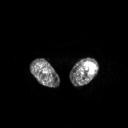
FDG PET of an extremity soft-tissue mass (from a PET/CT study), one axial slice; slice 196 of 267 in the series (ordered by position); 3.27 mm slice thickness; 128 × 128 image matrix, field of view 700 × 700 mm. Female patient, age 62 years. Case-level facts recorded for this patient, not image findings: histological type: undifferentiated – high grade; grade: high; site of the primary tumour: left thigh.
Outlined on this slice (expert contour drawn on MRI and transferred to this co-registered scan by the dataset authors):
- gross tumour volume including surrounding oedema: bounding box (x1, y1, x2, y2) in pixels: (85, 62, 95, 72)